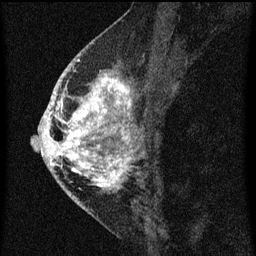
Breast MRI (dynamic contrast-enhanced), one sagittal slice; slice 29 of 60 in the series (ordered by position); dynamic contrast-enhanced series, image 2 of 3 at this slice position (ordered by acquisition); 1.5 T; TE 4.2 ms, TR 8 ms; 2 mm slice thickness; 256 × 256 image matrix, field of view 180 × 180 mm. Patient: female, 46 years.
Annotated regions visible in this slice (semi-automatic segmentation, software-assisted and operator-edited):
- analysis volume of interest (the breast-tissue region the enhancement analysis was run in; not a lesion): box from (x=48, y=68) to (x=134, y=195) px
- tumour enhancement mask (voxels above the 70 % enhancement threshold inside the analysis volume of interest): (x=48, y=68)–(x=133, y=189)